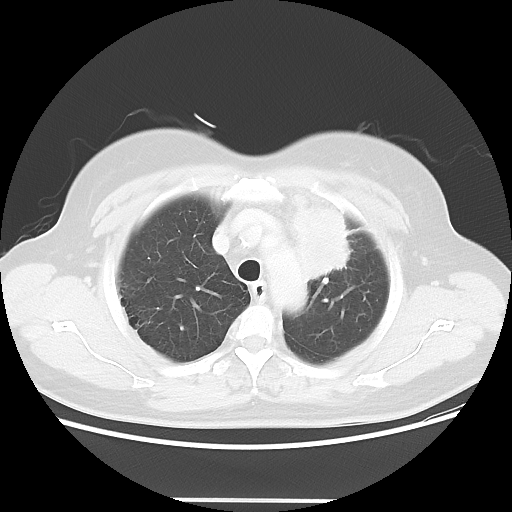
Chest CT, one axial slice. Position 43 of 52 along the scan axis. Lung window (W 1500 / L -600 HU). 5 mm slice thickness. 512 × 512 image matrix. Female patient, age 52 years. Case-level facts recorded for this patient, not image findings: clinical TNM (as recorded): T2 N3 M0.
Outlined on this slice (bounding box drawn by a radiologist):
- lung tumour (recorded histology: adenocarcinoma): box from (x=282, y=193) to (x=357, y=280) px